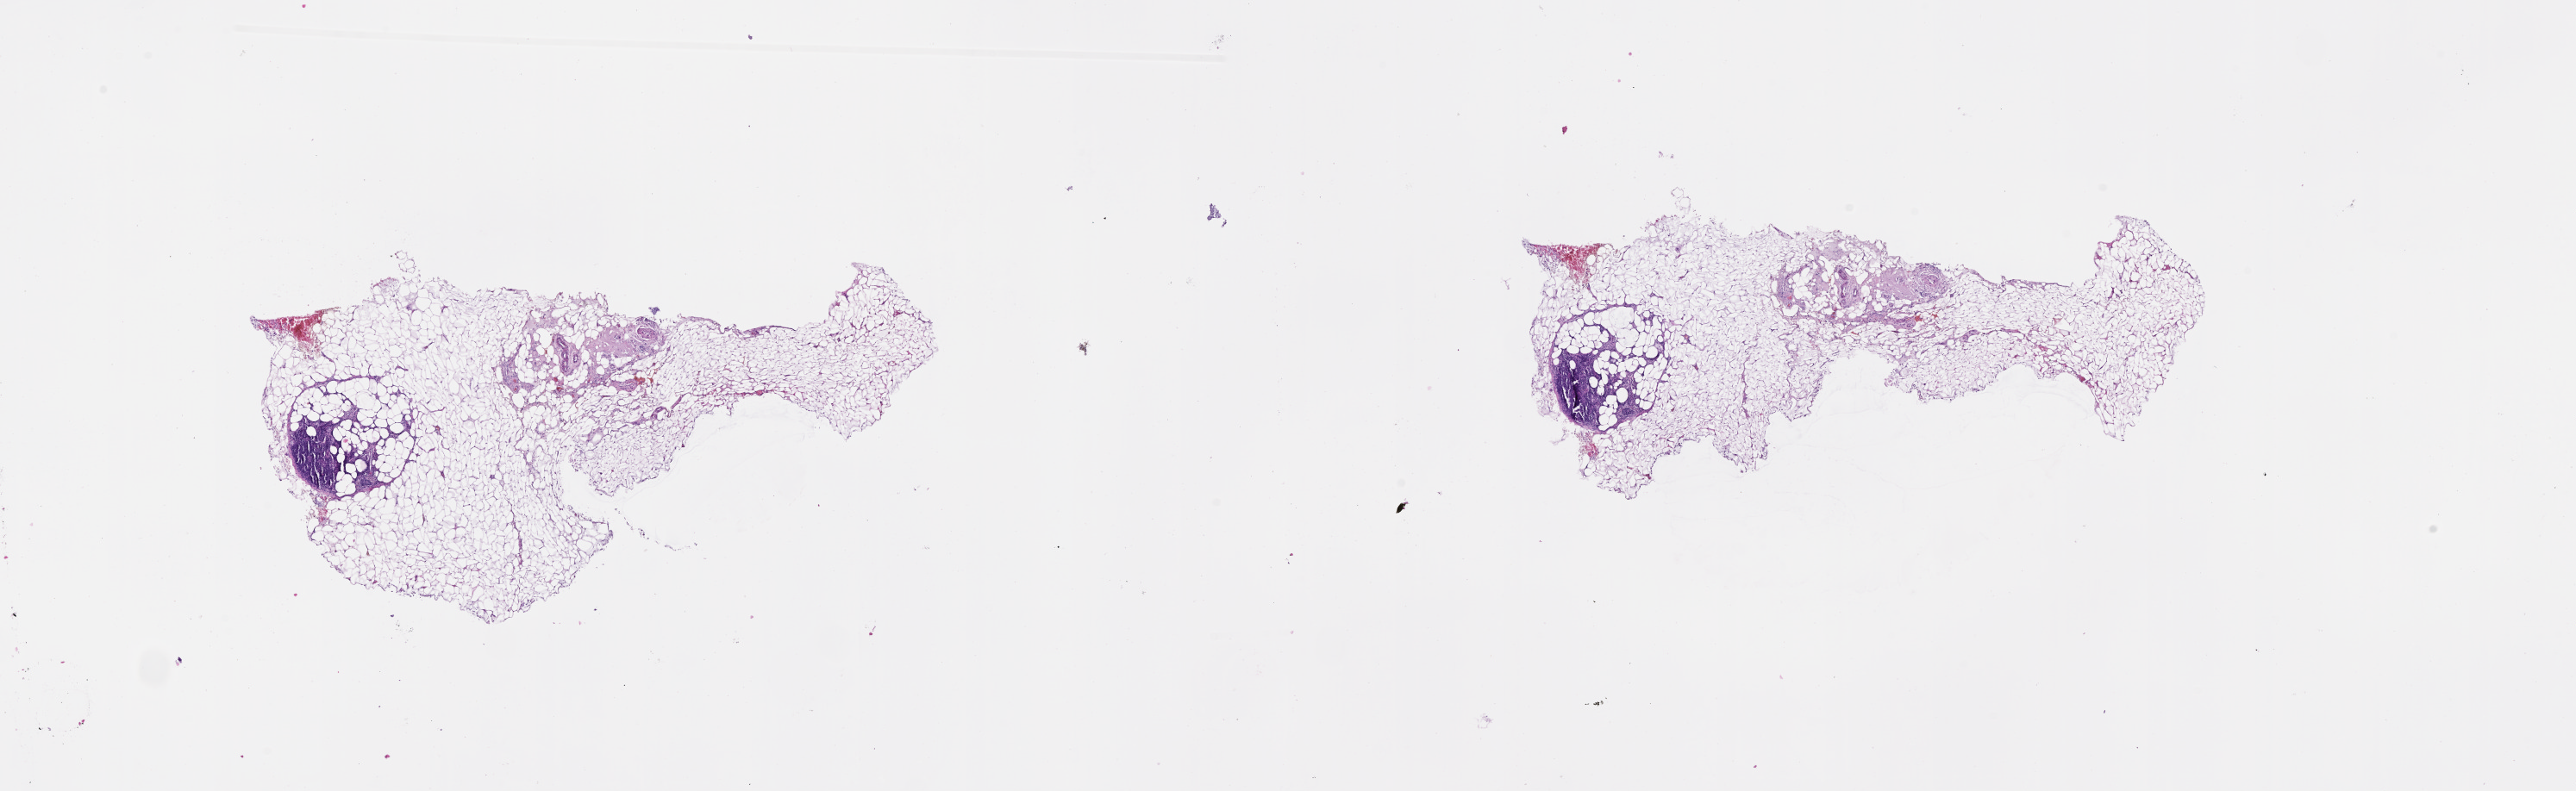
Digitized H&E tissue section (whole slide), a low-resolution overview of the entire scanned area, about 24.1 x 7.4 mm (from a 20x scan); normal (non-tumour) tissue sample, sampled site: lymph node. Patient: male, age 72 years.
This section: normal (non-tumour) tissue from the same patient. Patient diagnosis: Malignant melanoma, NOS.